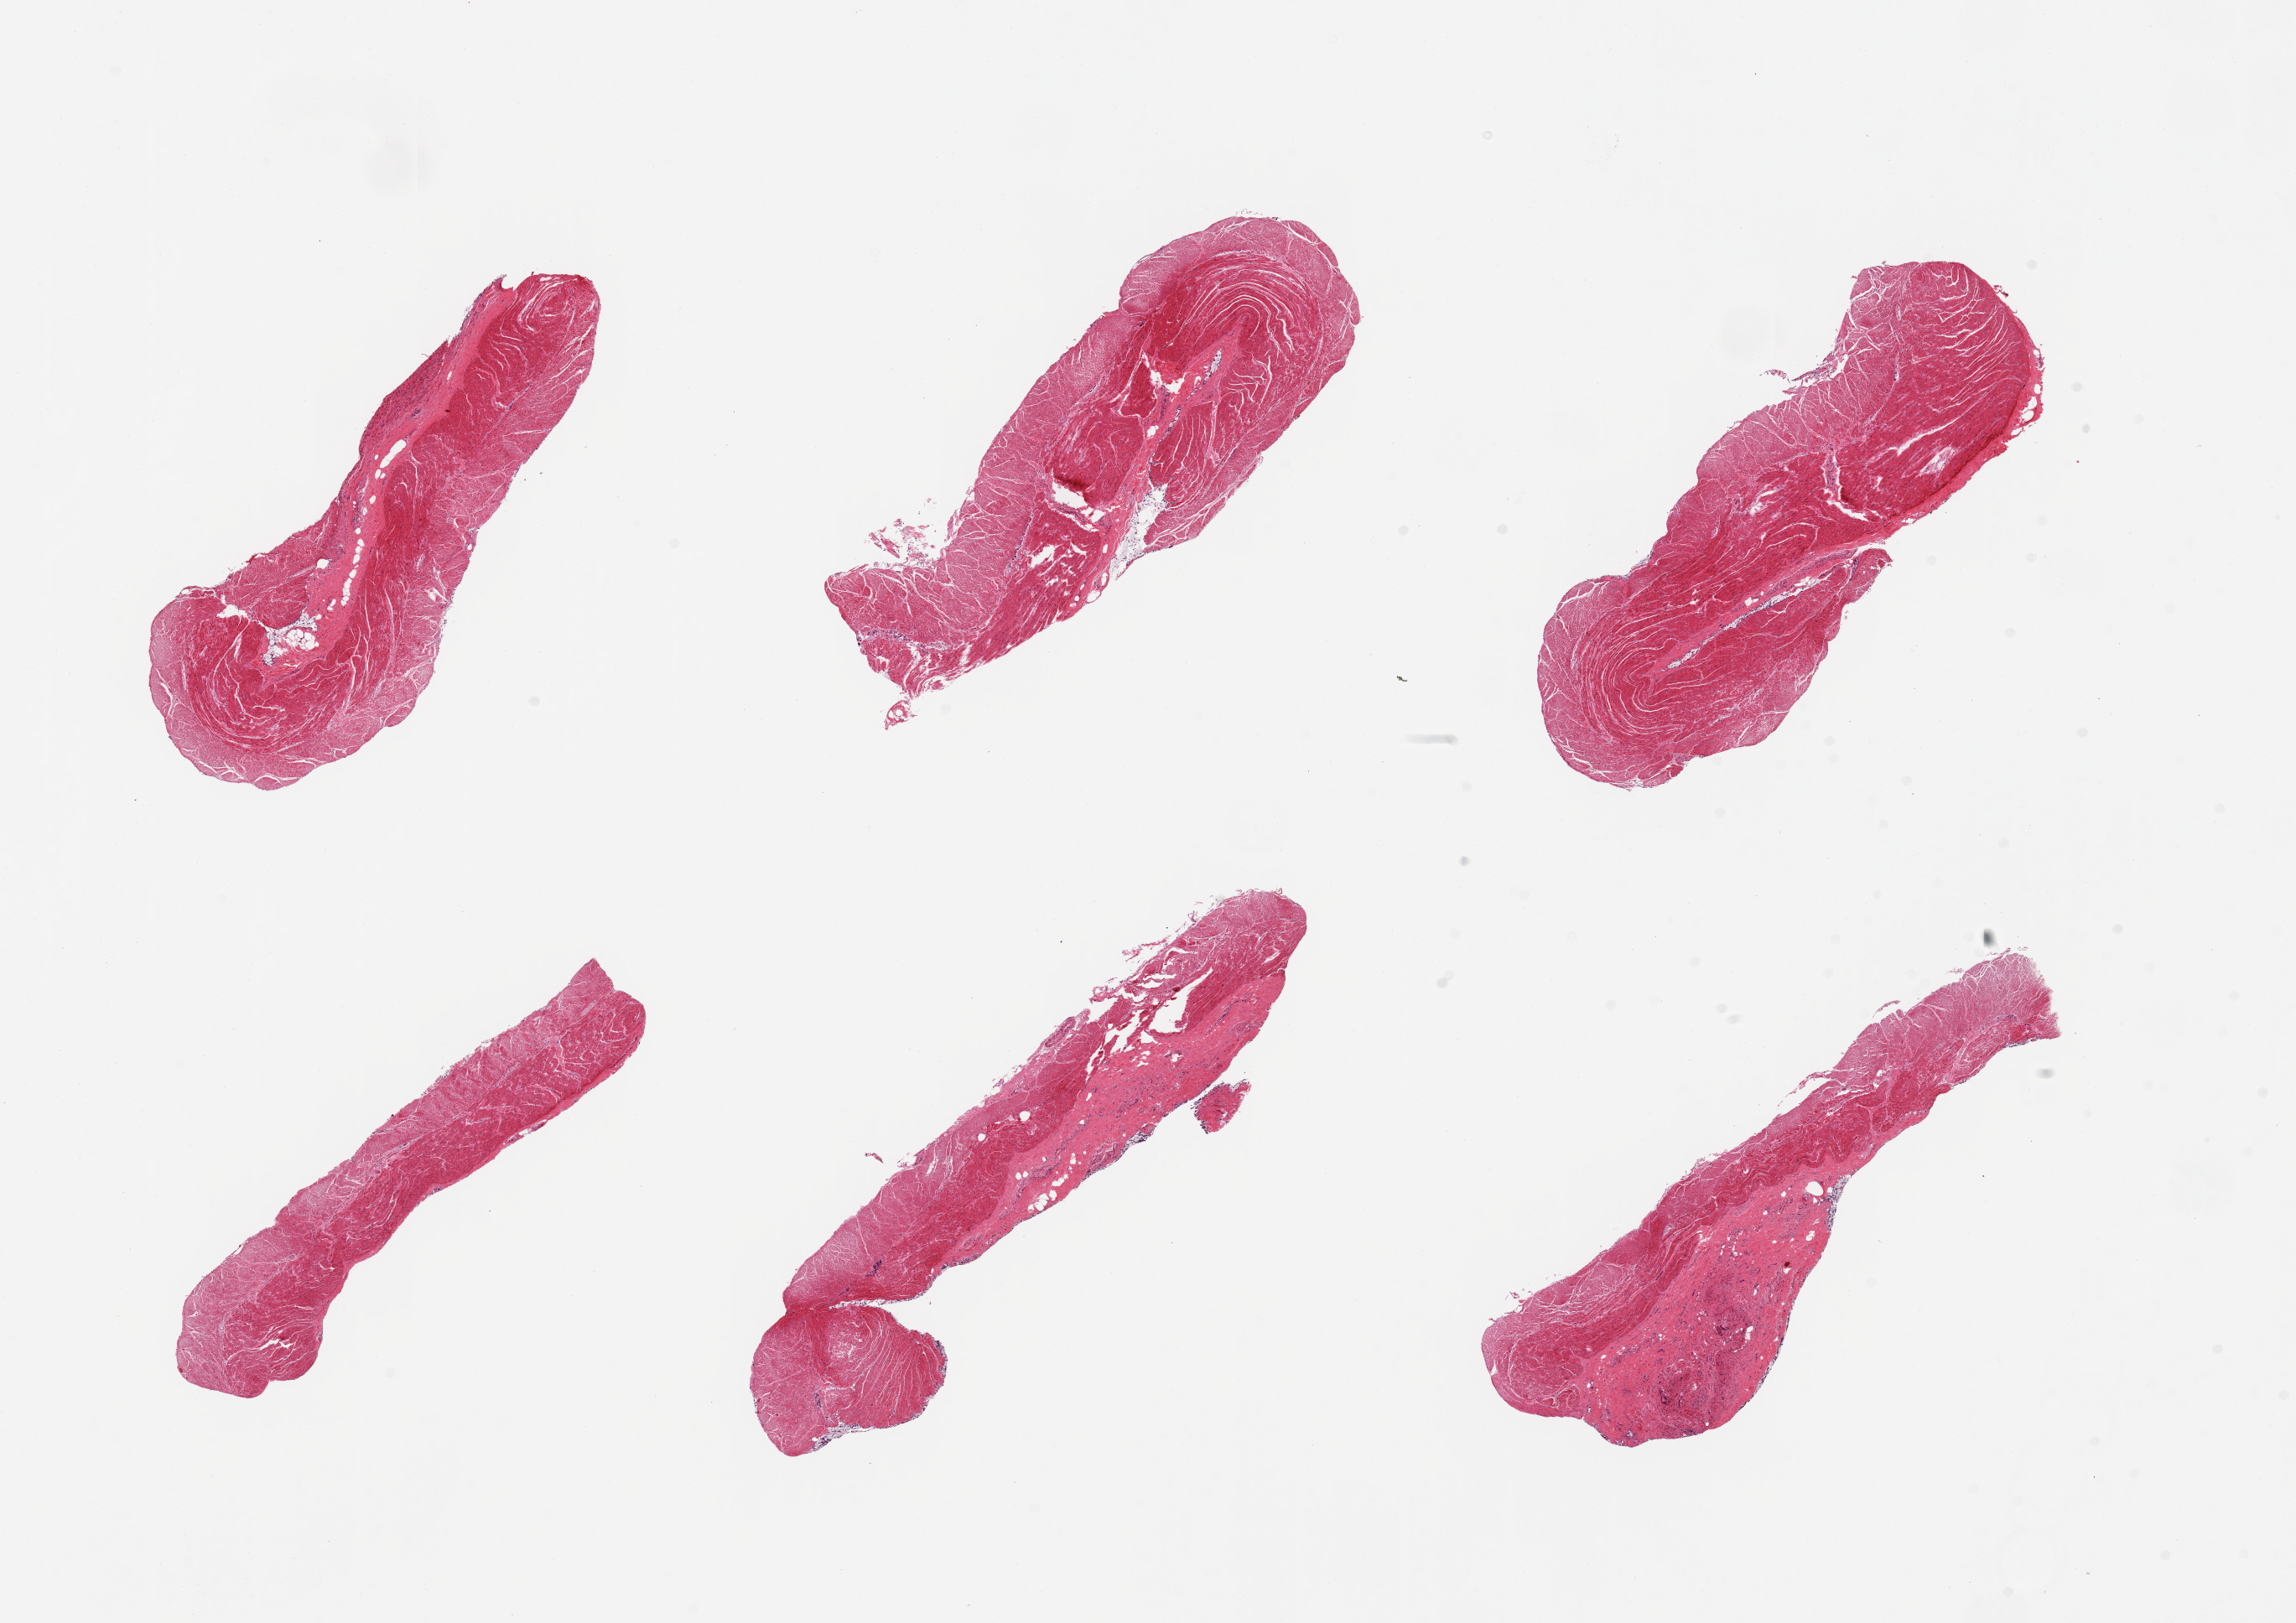
H&E whole-slide image, a low-resolution overview of the entire scanned area, about 21.7 x 15.3 mm (acquisition: 20x scan); PAXgene-fixed, paraffin-embedded tissue; sampled site (target tissue): sigmoid colon; tissue donor sample.
Reviewer comment on this tissue sample: 6 pieces, all target muscularis.